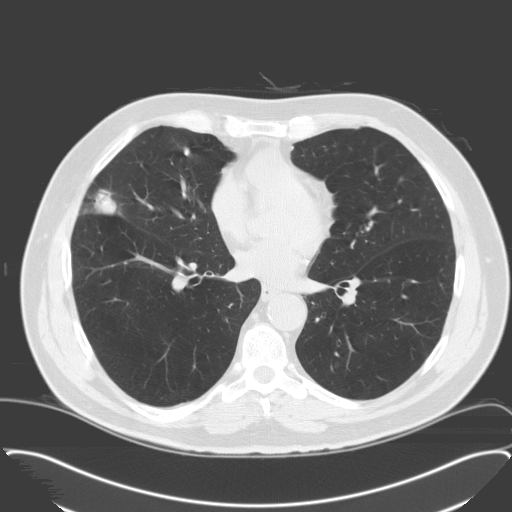
Low-dose screening chest CT, axial slice, third screening round (two years after baseline), lung window (W 1500 / L -600 HU), standard (soft-tissue) reconstruction kernel (C), 512 × 512 image matrix. Male, age 65 years at enrolment. Former smoker at enrolment.
- Expert reader's lesion annotation, bounding box <64,170,131,228> (left, top, right, bottom; pixels).
- Screening reader's record for this exam (one nodule recorded; not confirmed to be the boxed lesion): non-calcified nodule or mass ≥4 mm, right middle lobe, 28 × 23 mm, spiculated (stellate) margins, soft tissue attenuation, pre-existing on the prior screen: no.
- Official screen result: positive, other.
- Participant outcome: lung cancer diagnosed 25 days after this screen — adenocarcinoma, NOS, right middle lobe, moderately differentiated (G2), stage IA (AJCC 6th edition), 25 mm at pathology.